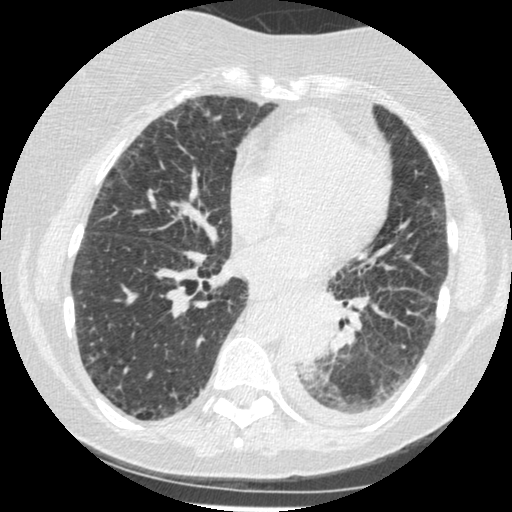
Low-dose screening chest CT, one axial slice. Slice 97 of 341 in the series (ordered by position). Lung window (W 1500 / L -600 HU). 1.25 mm slice thickness. 512 × 512 image matrix.
Structures marked on this image (expert manual segmentation):
- lesion 1 (tumor, lower lobe of left lung): box from (x=287, y=309) to (x=333, y=363) px